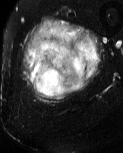
MRI of an extremity soft-tissue mass, one axial slice. Slice 17 of 60 in the series (ordered by position). T2-weighted fat-saturated. MR volume resampled by the dataset authors to the PET/CT grid (not the native acquisition matrix). 3.27 mm slice thickness. 123 × 153 image matrix, field of view 120 × 149 mm. Male patient. From the clinical record (not read from this slice): histological type: pleiomorphic liposarcoma; grade: high; site of the primary tumour: left thigh.
Outlined on this slice (expert contour drawn on MRI and transferred to this co-registered scan by the dataset authors):
- gross tumour volume including surrounding oedema: bounding box [x1, y1, x2, y2] px = [24, 18, 103, 103]
- gross tumour volume (mass): [29, 45, 85, 98]